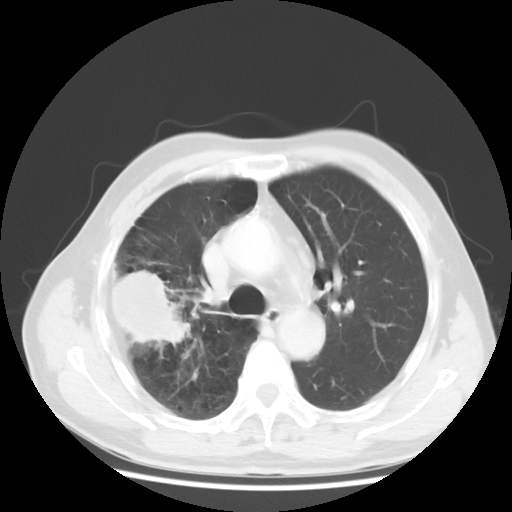
Chest CT, one axial slice; reconstruction kernel STANDARD; lung window (W 1500 / L -600 HU); 5 mm slice thickness; 512 × 512 image matrix, field of view 360 × 360 mm. Patient: male, 69 years. Case-level facts recorded for this patient, not image findings: clinical TNM (as recorded): T3 N0 M0; histopathological grade: G3.
Structures marked on this image (bounding box drawn by a radiologist):
- lung tumour (recorded histology: adenocarcinoma): bounding box <111,262,198,348> (left, top, right, bottom; pixels)